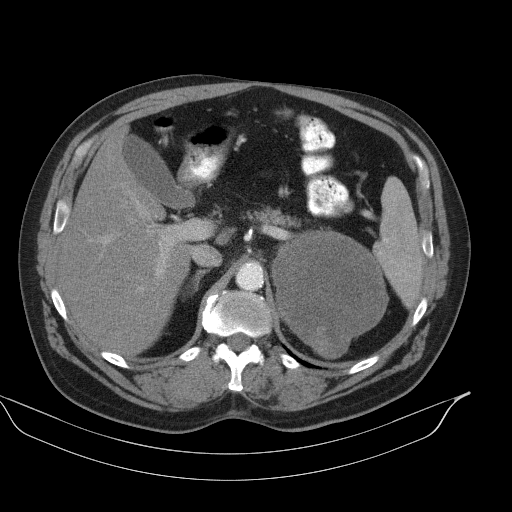
Contrast-enhanced abdominal CT, one axial slice. Position 69 of 92 along the scan axis. Intravenous contrast given. Soft-tissue window (W 400 / L 40 HU). 5 mm slice thickness. 512 × 512 image matrix, field of view 449 × 449 mm. Male patient, age 56 years. Case-level facts recorded for this patient, not image findings: diagnosis: adrenocortical carcinoma; tumour side: left adrenal; tumour size at pathology: 15 cm; Ki-67 index: 35 %; stage (as recorded): 4.
Outlined on this slice (semi-automatically segmented with operator editing):
- mass: bounding box (x1, y1, x2, y2) in pixels: (274, 232, 386, 358)